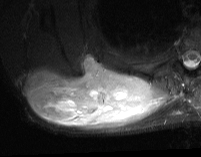
MRI of an extremity soft-tissue mass, one axial slice; slice 28 of 74 in the series (ordered by position); STIR; MR volume resampled by the dataset authors to the PET/CT grid (not the native acquisition matrix); 3.27 mm slice thickness; 201 × 157 image matrix, field of view 196 × 153 mm. Male patient. From the clinical record (not read from this slice): histological type: pleiomorphic spindle cell undifferentiated; grade: high; site of the primary tumour: right parascapusular.
Outlined on this slice (expert contour drawn on MRI and transferred to this co-registered scan by the dataset authors):
- gross tumour volume including surrounding oedema: bounding box (x1, y1, x2, y2) in pixels: (26, 57, 169, 131)
- gross tumour volume (mass): (26, 57, 152, 127)